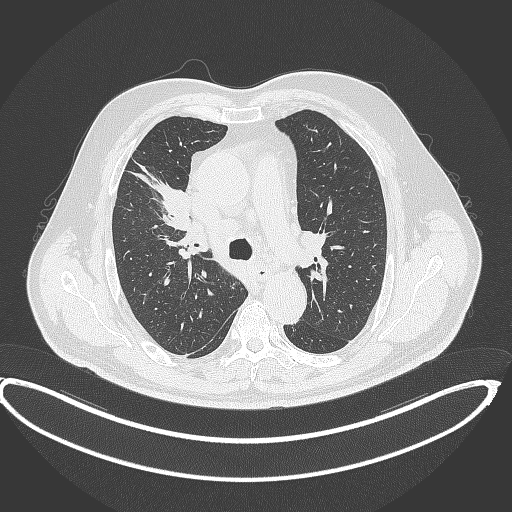
Chest CT, one axial slice. Position 274 of 390 along the scan axis. Lung window (W 1500 / L -600 HU). 512 × 512 image matrix, field of view 448 × 448 mm. Patient: male, 62 years. From the clinical record (not read from this slice): clinical TNM (as recorded): T1c N3 M1c.
Annotated regions visible in this slice (rectangle marked by the reading radiologist):
- lung tumour (recorded histology: adenocarcinoma): bounding box [x1, y1, x2, y2] px = [151, 182, 194, 237]